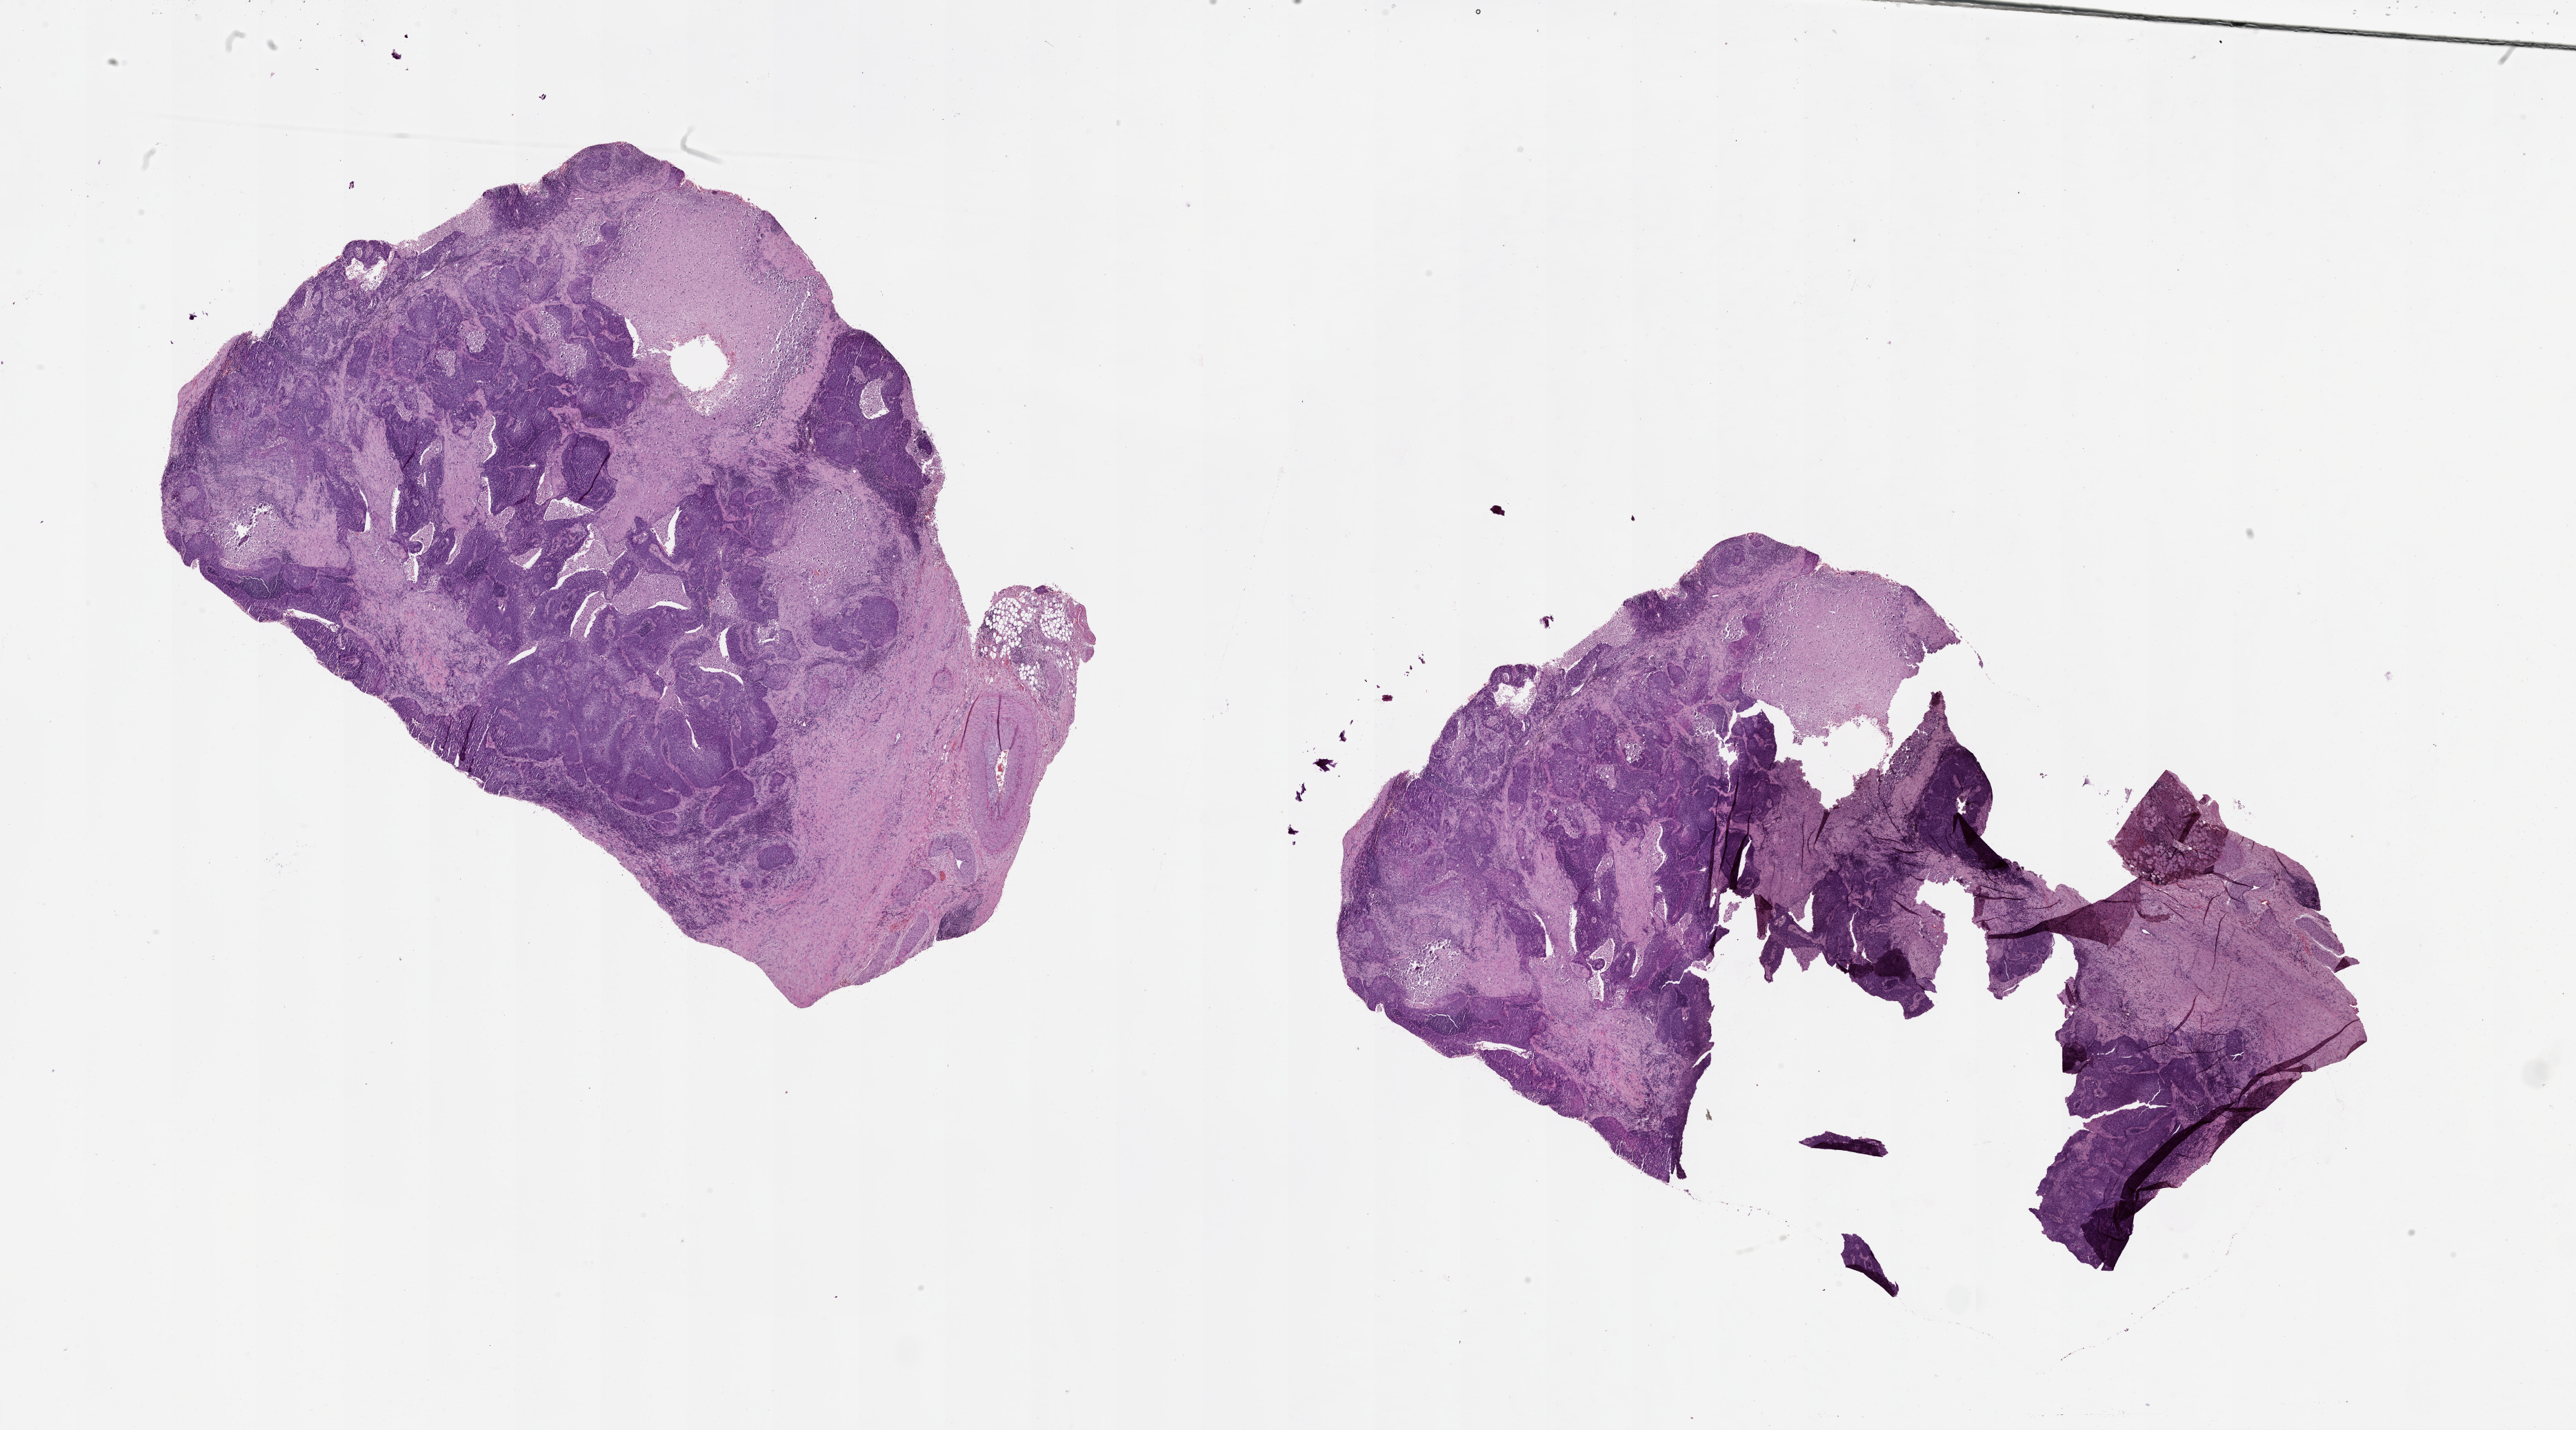
Digitized H&E tissue section (whole slide), low-resolution overview of the scanned area, about 30.1 x 16.7 mm (slide scanned at 20x); lung, tumour tissue. 53-year-old male patient.
Patient diagnosis (cohort enrolment): squamous cell carcinoma (lung).